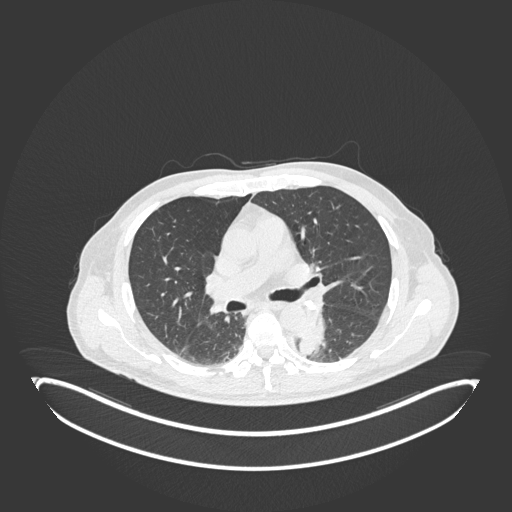
Chest CT, one axial slice. Slice 123 of 251 in the series (ordered by position). 120 kVp. Lung window (W 1500 / L -600 HU). 512 × 512 image matrix. Patient: male, 72 years. Case-level facts recorded for this patient, not image findings: clinical TNM (as recorded): T2b N0 M1.
Annotated regions visible in this slice (bounding box drawn by a radiologist):
- lung tumour (recorded histology: adenocarcinoma): bounding box (x1, y1, x2, y2) in pixels: (299, 311, 327, 359)